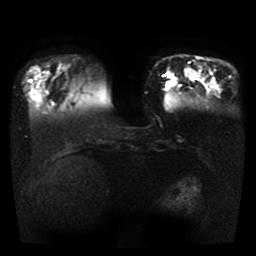
Breast MRI, one axial slice; position 10 of 41 along the scan axis; diffusion-weighted series; image 2 of 4 stored at this slice position (different b-values; order by instance number); 1.5 T; 5 mm slice thickness; 256 × 256 image matrix, field of view 330 × 330 mm. Female patient.
Annotated regions visible in this slice (outlined manually by an expert reader):
- tumour on diffusion-weighted imaging: box from (x=165, y=81) to (x=177, y=88) px